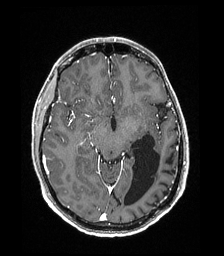
Brain MRI from a brain-tumour surgery series, one axial slice; slice 105 of 192 in the series (ordered by position); T1-weighted post-contrast; 1 mm slice thickness; 224 × 256 image matrix, field of view 224 × 256 mm. From the clinical record (not read from this slice): histopathology: Low grade glioma; IDH mutation: no.
Outlined on this slice (manually delineated by an expert):
- previous resection cavity: bounding box <124,134,160,206> (left, top, right, bottom; pixels)